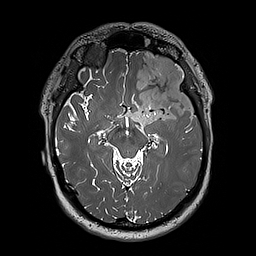
Brain MRI from a brain-tumour surgery series, one axial slice. 1 mm slice thickness. 256 × 256 image matrix, field of view 250 × 250 mm. Case-level facts recorded for this patient, not image findings: histopathology: Oligodendroglioma; WHO grade: 3.
Outlined on this slice (outlined manually by an expert reader):
- tumour: bounding box [x1, y1, x2, y2] px = [124, 53, 197, 125]